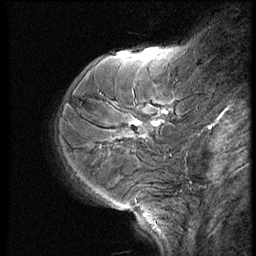
Breast MRI (dynamic contrast-enhanced), one sagittal slice; slice 16 of 52 in the series (ordered by position); dynamic contrast-enhanced series, image 2 of 3 at this slice position (ordered by acquisition); 1.5 T; TE 4.2 ms, TR 9 ms; 256 × 256 image matrix, field of view 180 × 180 mm. Female patient, age 62 years. From the clinical record (not read from this slice): setting: breast cancer imaged before/during neoadjuvant chemotherapy; receptor status: HR-positive, HER2-negative.
Structures marked on this image (semi-automatic segmentation, software-assisted and operator-edited):
- analysis volume of interest (the breast-tissue region the enhancement analysis was run in; not a lesion): box from (x=67, y=94) to (x=182, y=177) px
- tumour enhancement mask (voxels above the 140 % enhancement threshold inside the analysis volume of interest): (x=135, y=111)–(x=167, y=125)